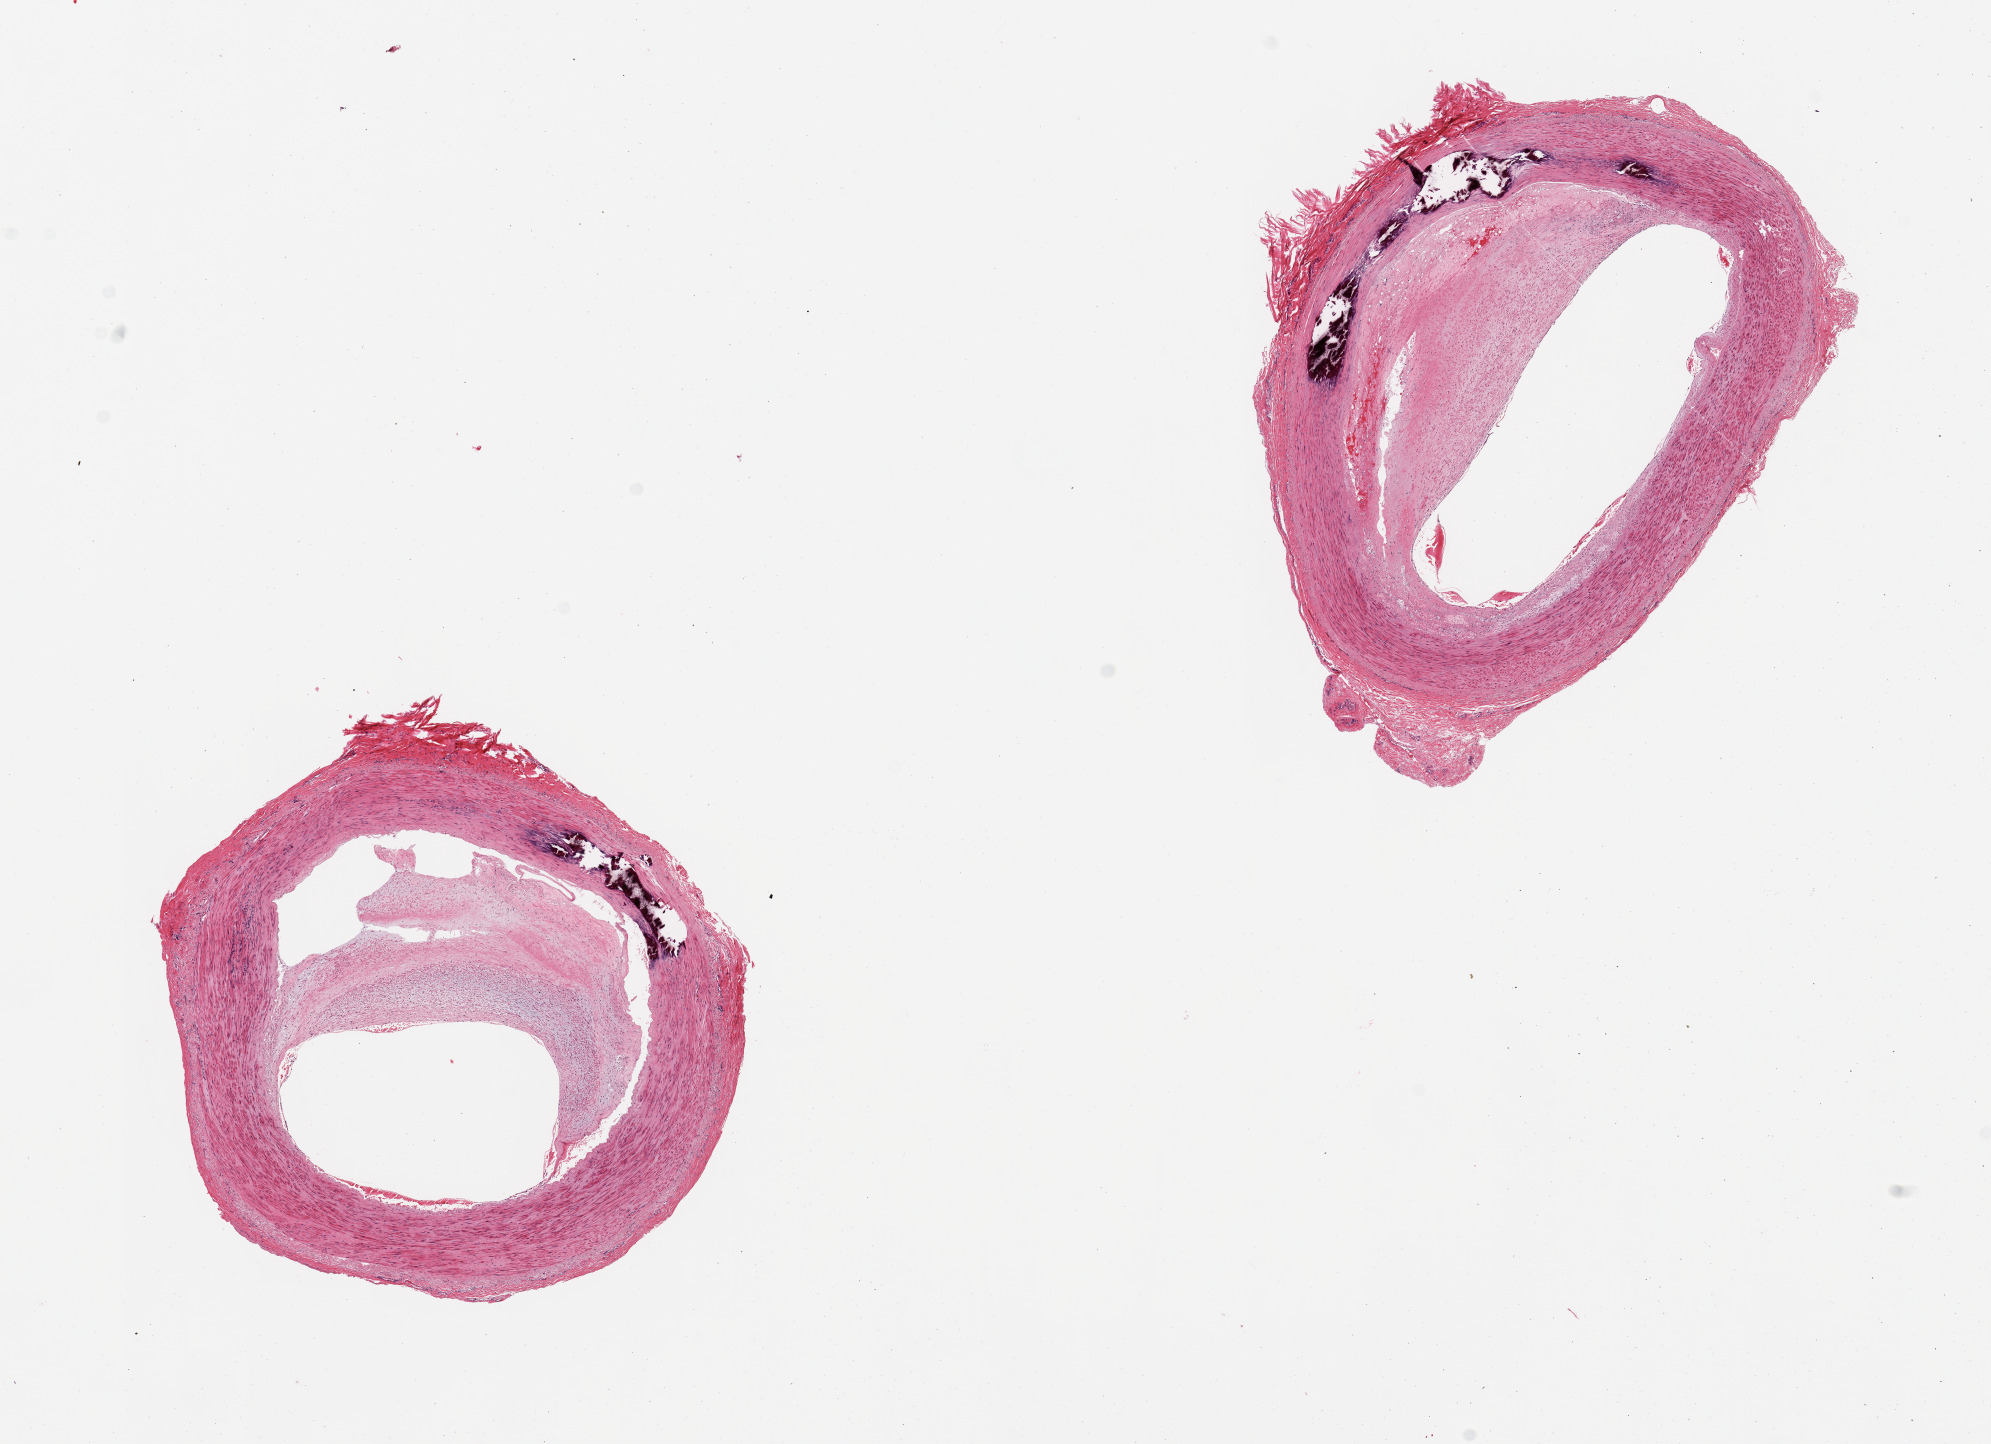
H&E whole-slide image — low-resolution overview of the scanned area, about 15.8 x 11.4 mm. PAXgene-fixed paraffin-embedded (PFPE) section. Section of tibial artery (target tissue). Tissue donor sample.
- pathologist's review note for this sample: 2 pieces; large eccentric atheromatous plaques; moderate medial calcification; well trimmed